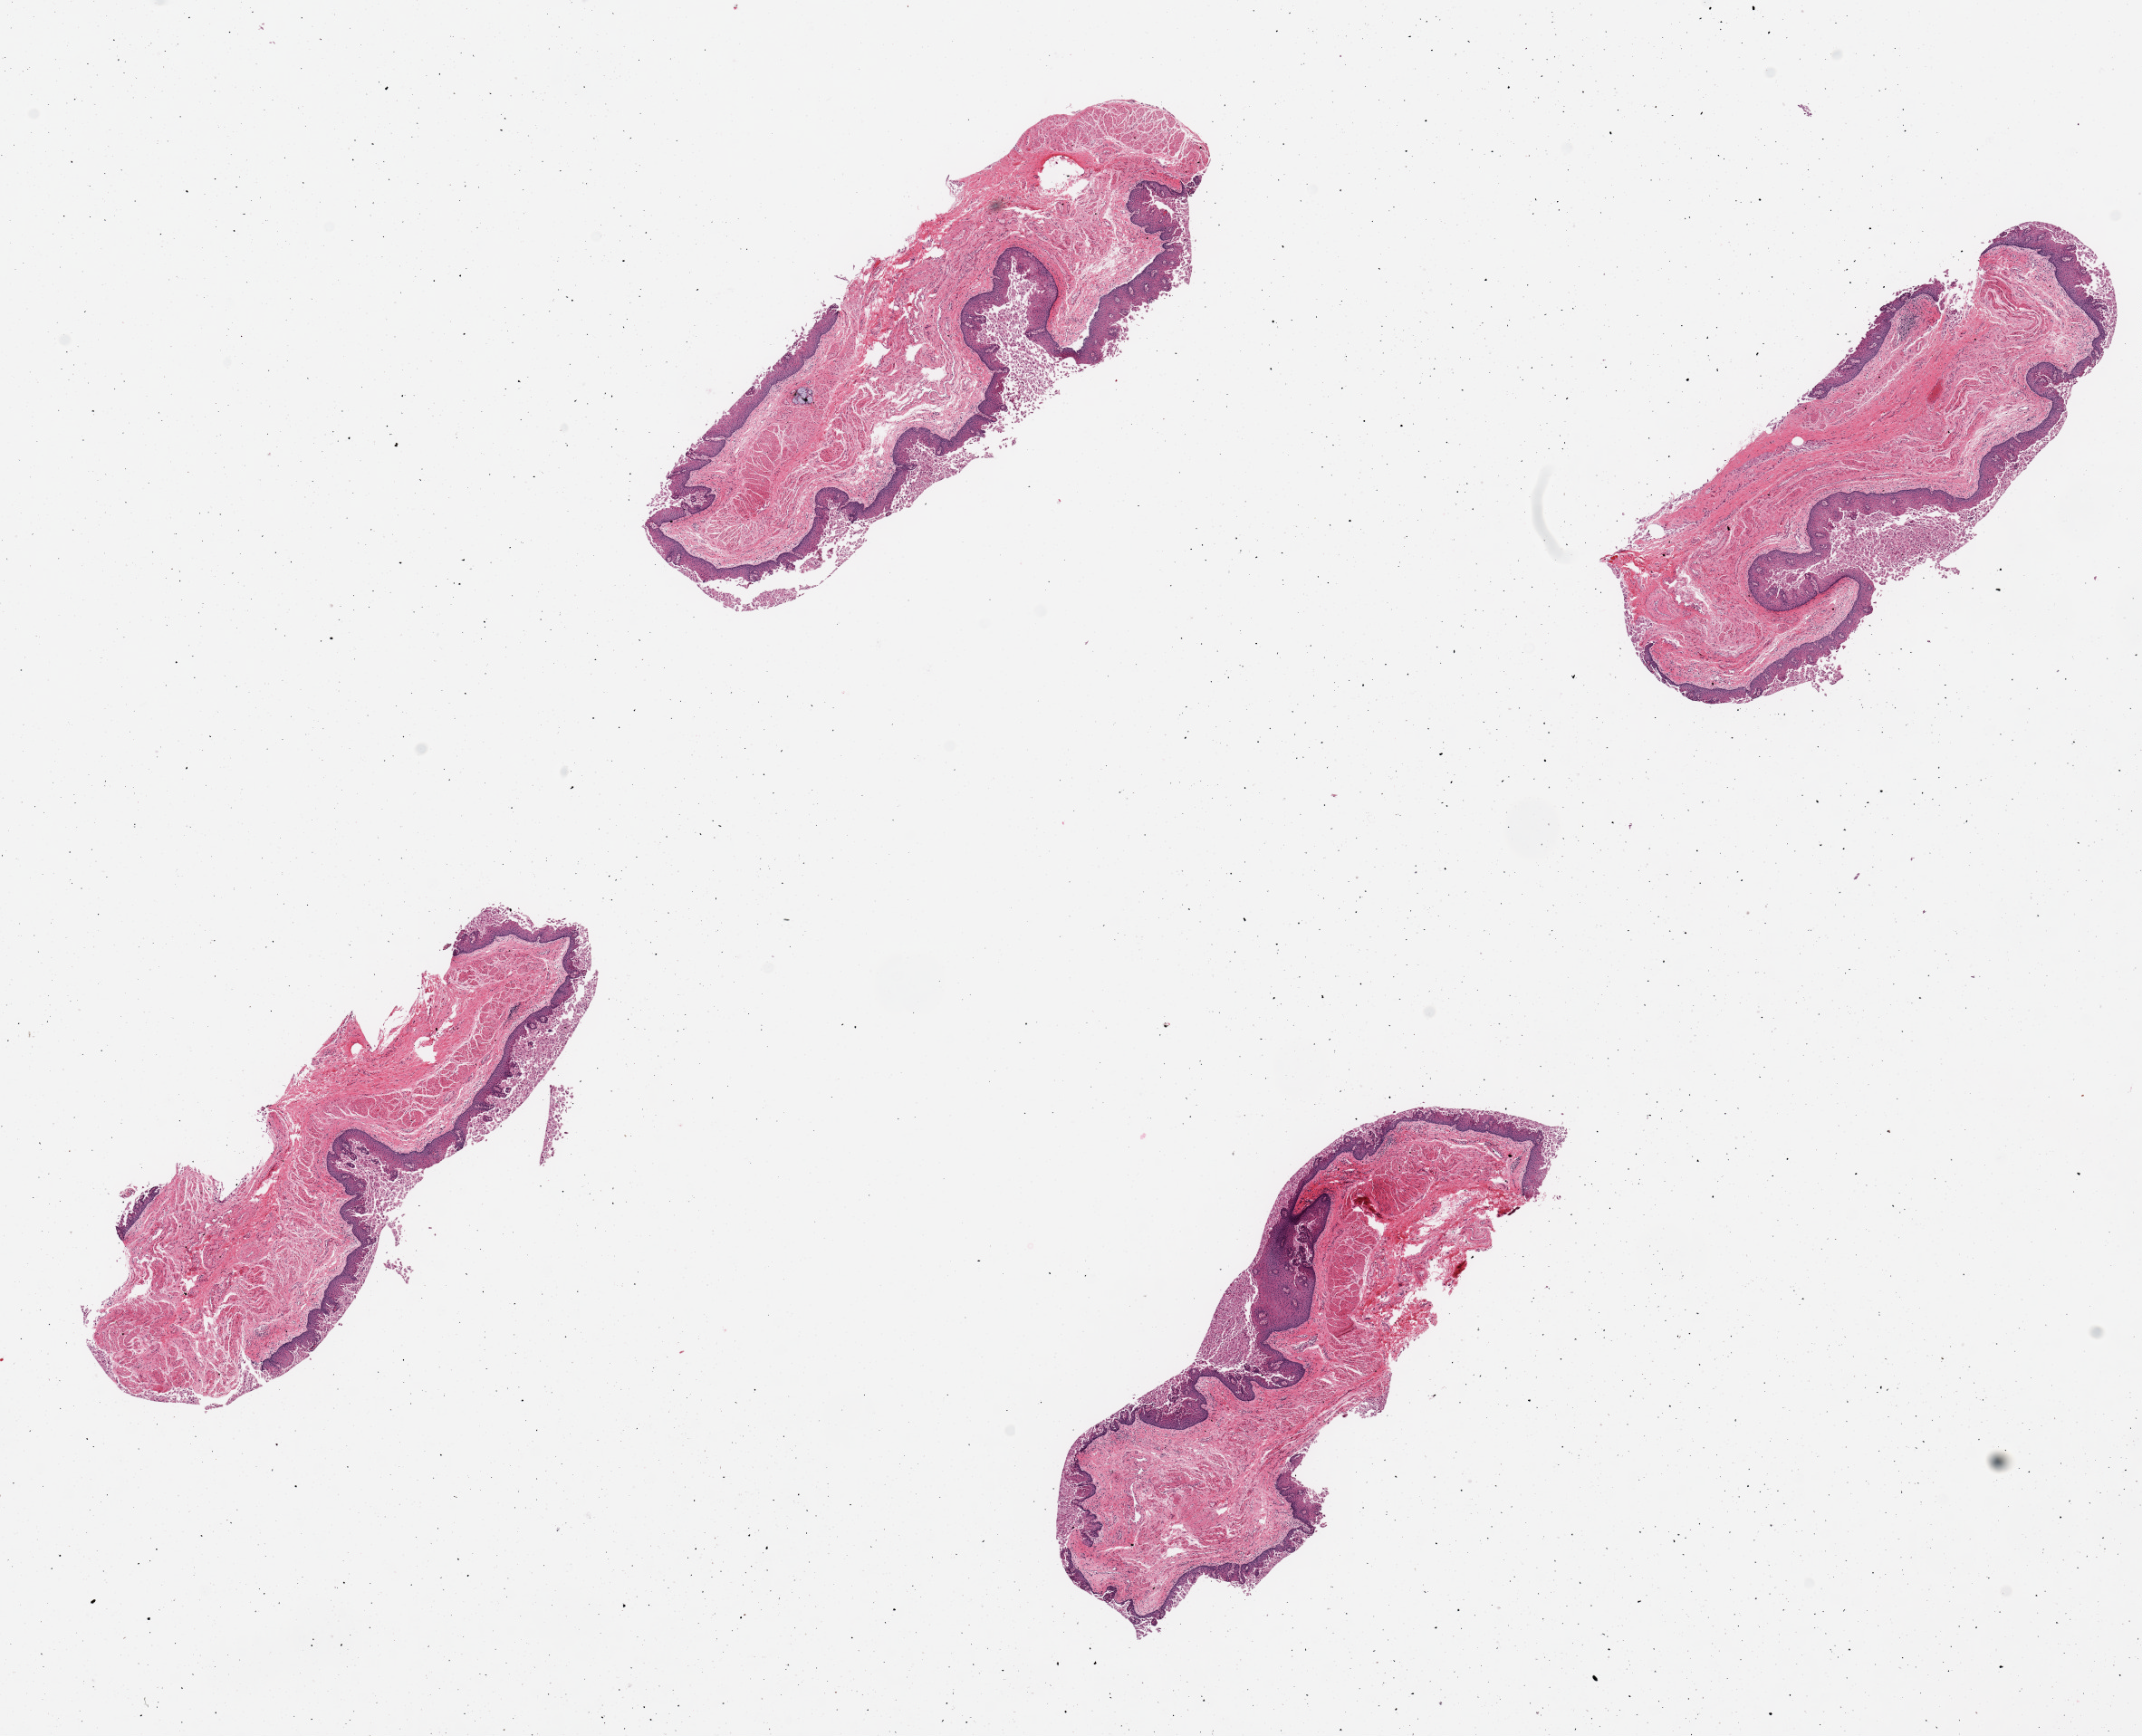
Digitized haematoxylin and eosin-stained section, brightfield, shown as a low-resolution overview of the whole scanned area (about 18.7 x 15.2 mm); PAXgene-fixed paraffin-embedded (PFPE) section; target tissue: esophageal mucous membrane; tissue donor sample.
Reviewer comment on this tissue sample: 4 pieces; moderate sloughing of squamous epithelium.